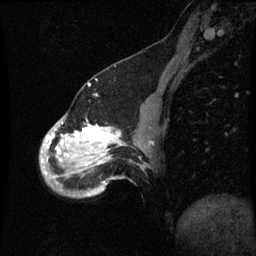
Breast MRI (dynamic contrast-enhanced), one sagittal slice; position 17 of 60 along the scan axis; dynamic contrast-enhanced series, image 2 of 3 at this slice position (ordered by acquisition); 1.5 T; TE 4.2 ms, TR 8.9 ms; 2 mm slice thickness; 256 × 256 image matrix, field of view 200 × 200 mm. Patient: female, 49 years. Case-level facts recorded for this patient, not image findings: setting: breast cancer imaged before/during neoadjuvant chemotherapy; receptor status: HR-positive, HER2-negative.
Structures marked on this image (semi-automatically segmented with operator editing):
- analysis volume of interest (the breast-tissue region the enhancement analysis was run in; not a lesion): bounding box [x1, y1, x2, y2] px = [40, 112, 147, 199]
- tumour enhancement mask (voxels above the 70 % enhancement threshold inside the analysis volume of interest): [46, 126, 119, 161]